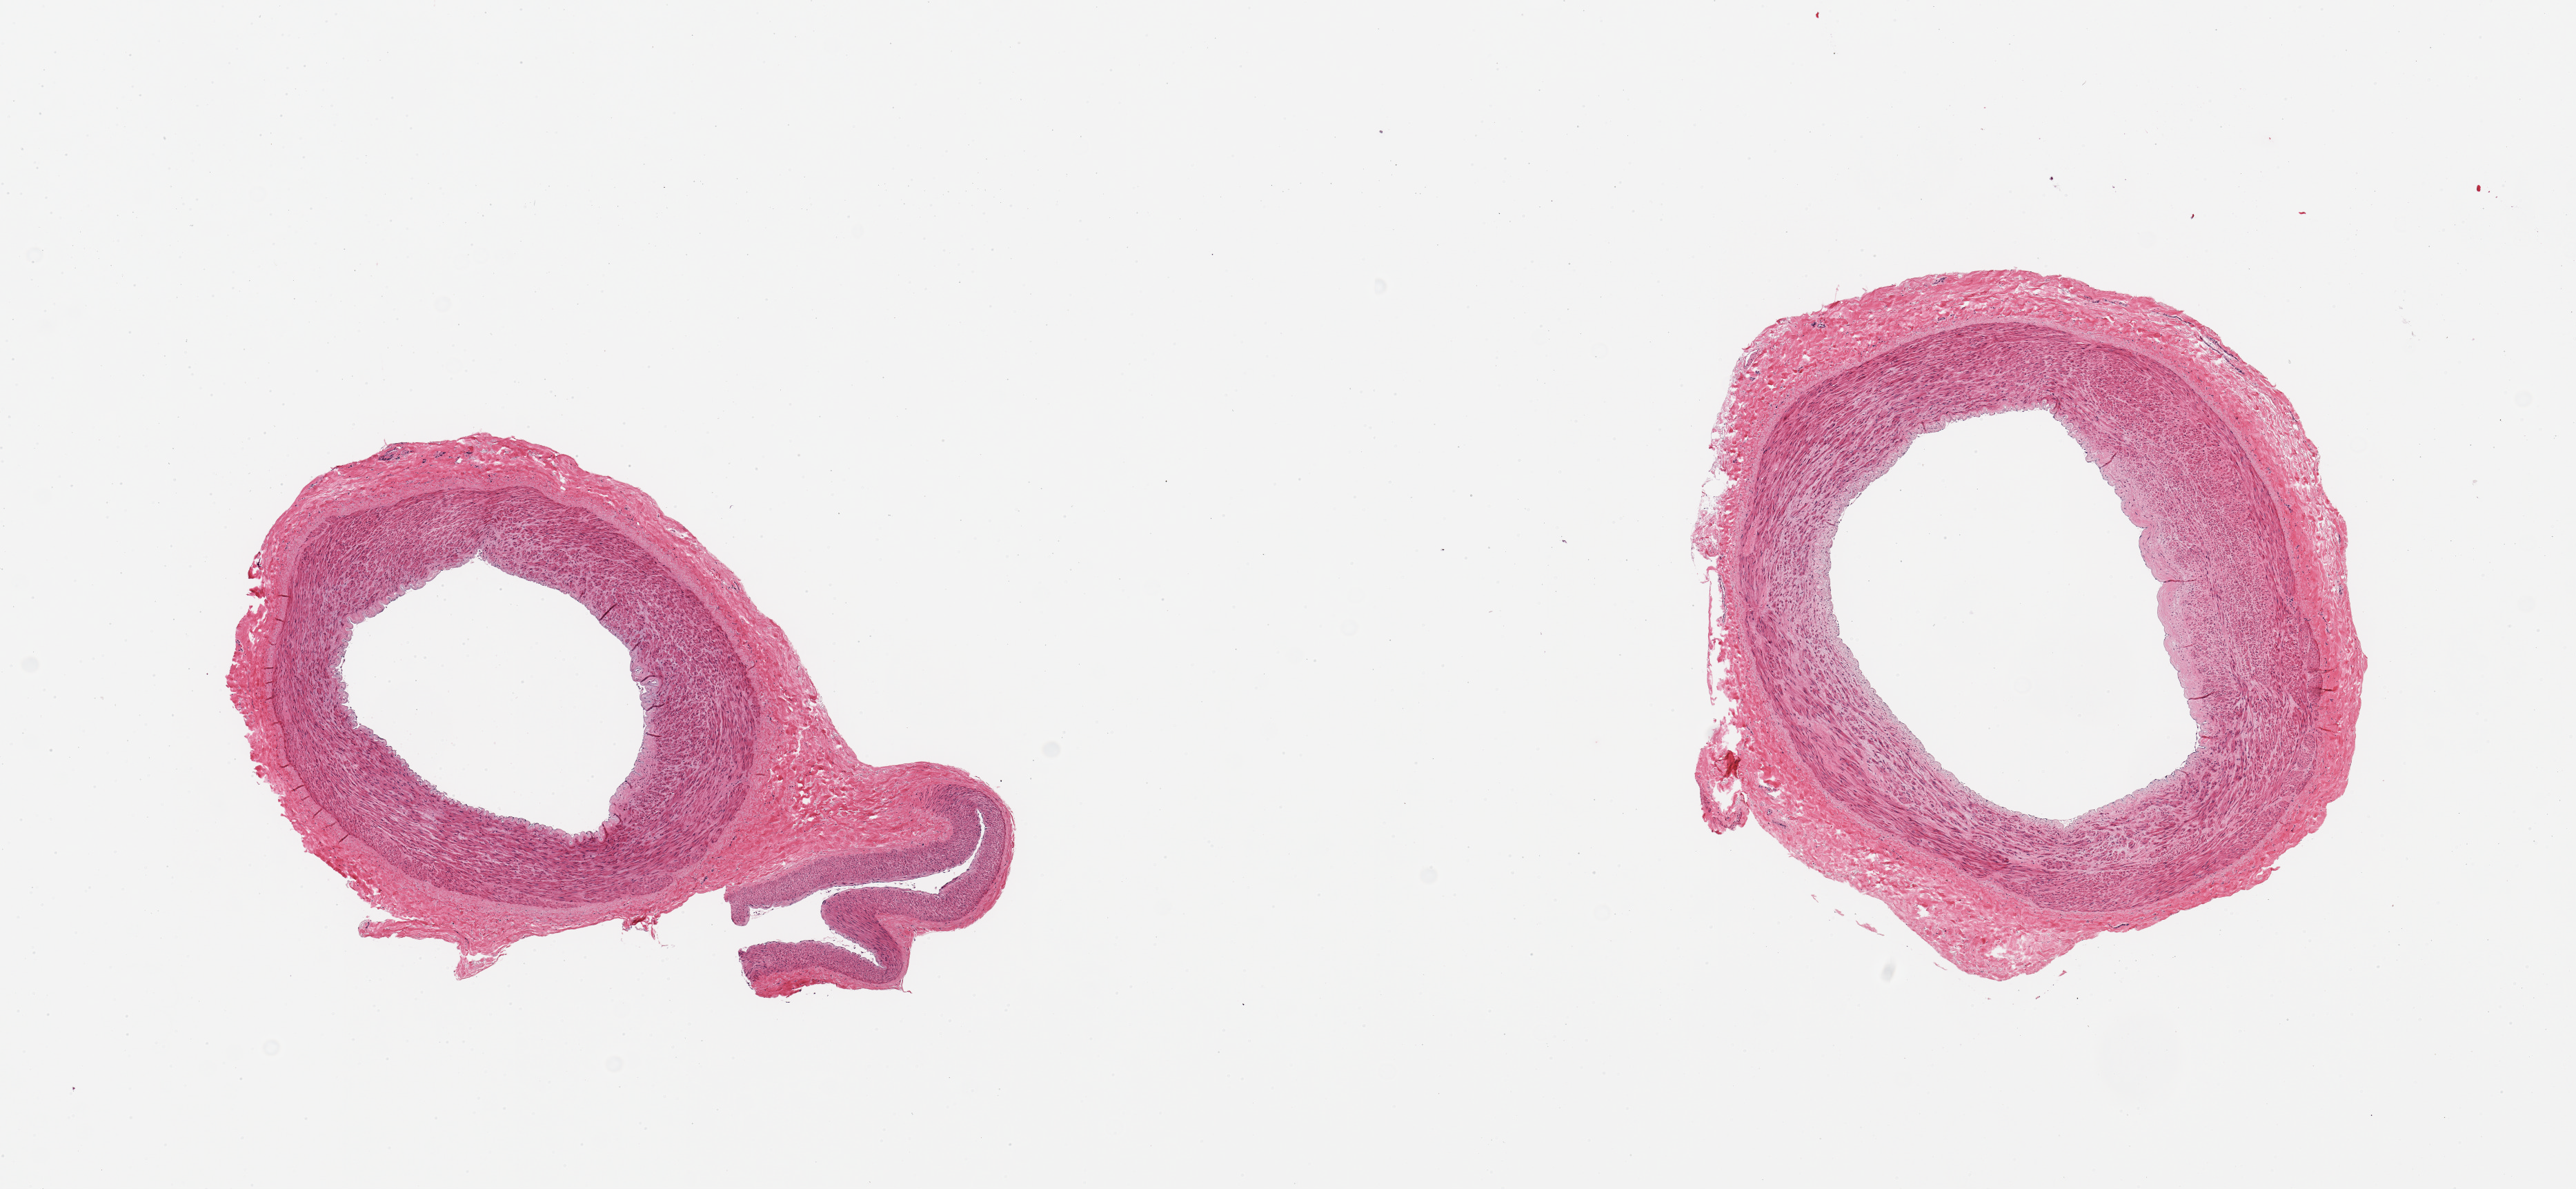
Digitized hematoxylin and eosin (H&E)-stained section, brightfield — low-resolution overview of the scanned area, about 14.8 x 6.8 mm (from a 20x scan), PAXgene-fixed paraffin-embedded (PFPE) section, target tissue: tibial artery, tissue donor sample. Female donor.
Reviewer comment on this tissue sample: 2 pieces; ~0.5mm of attached adventitia.